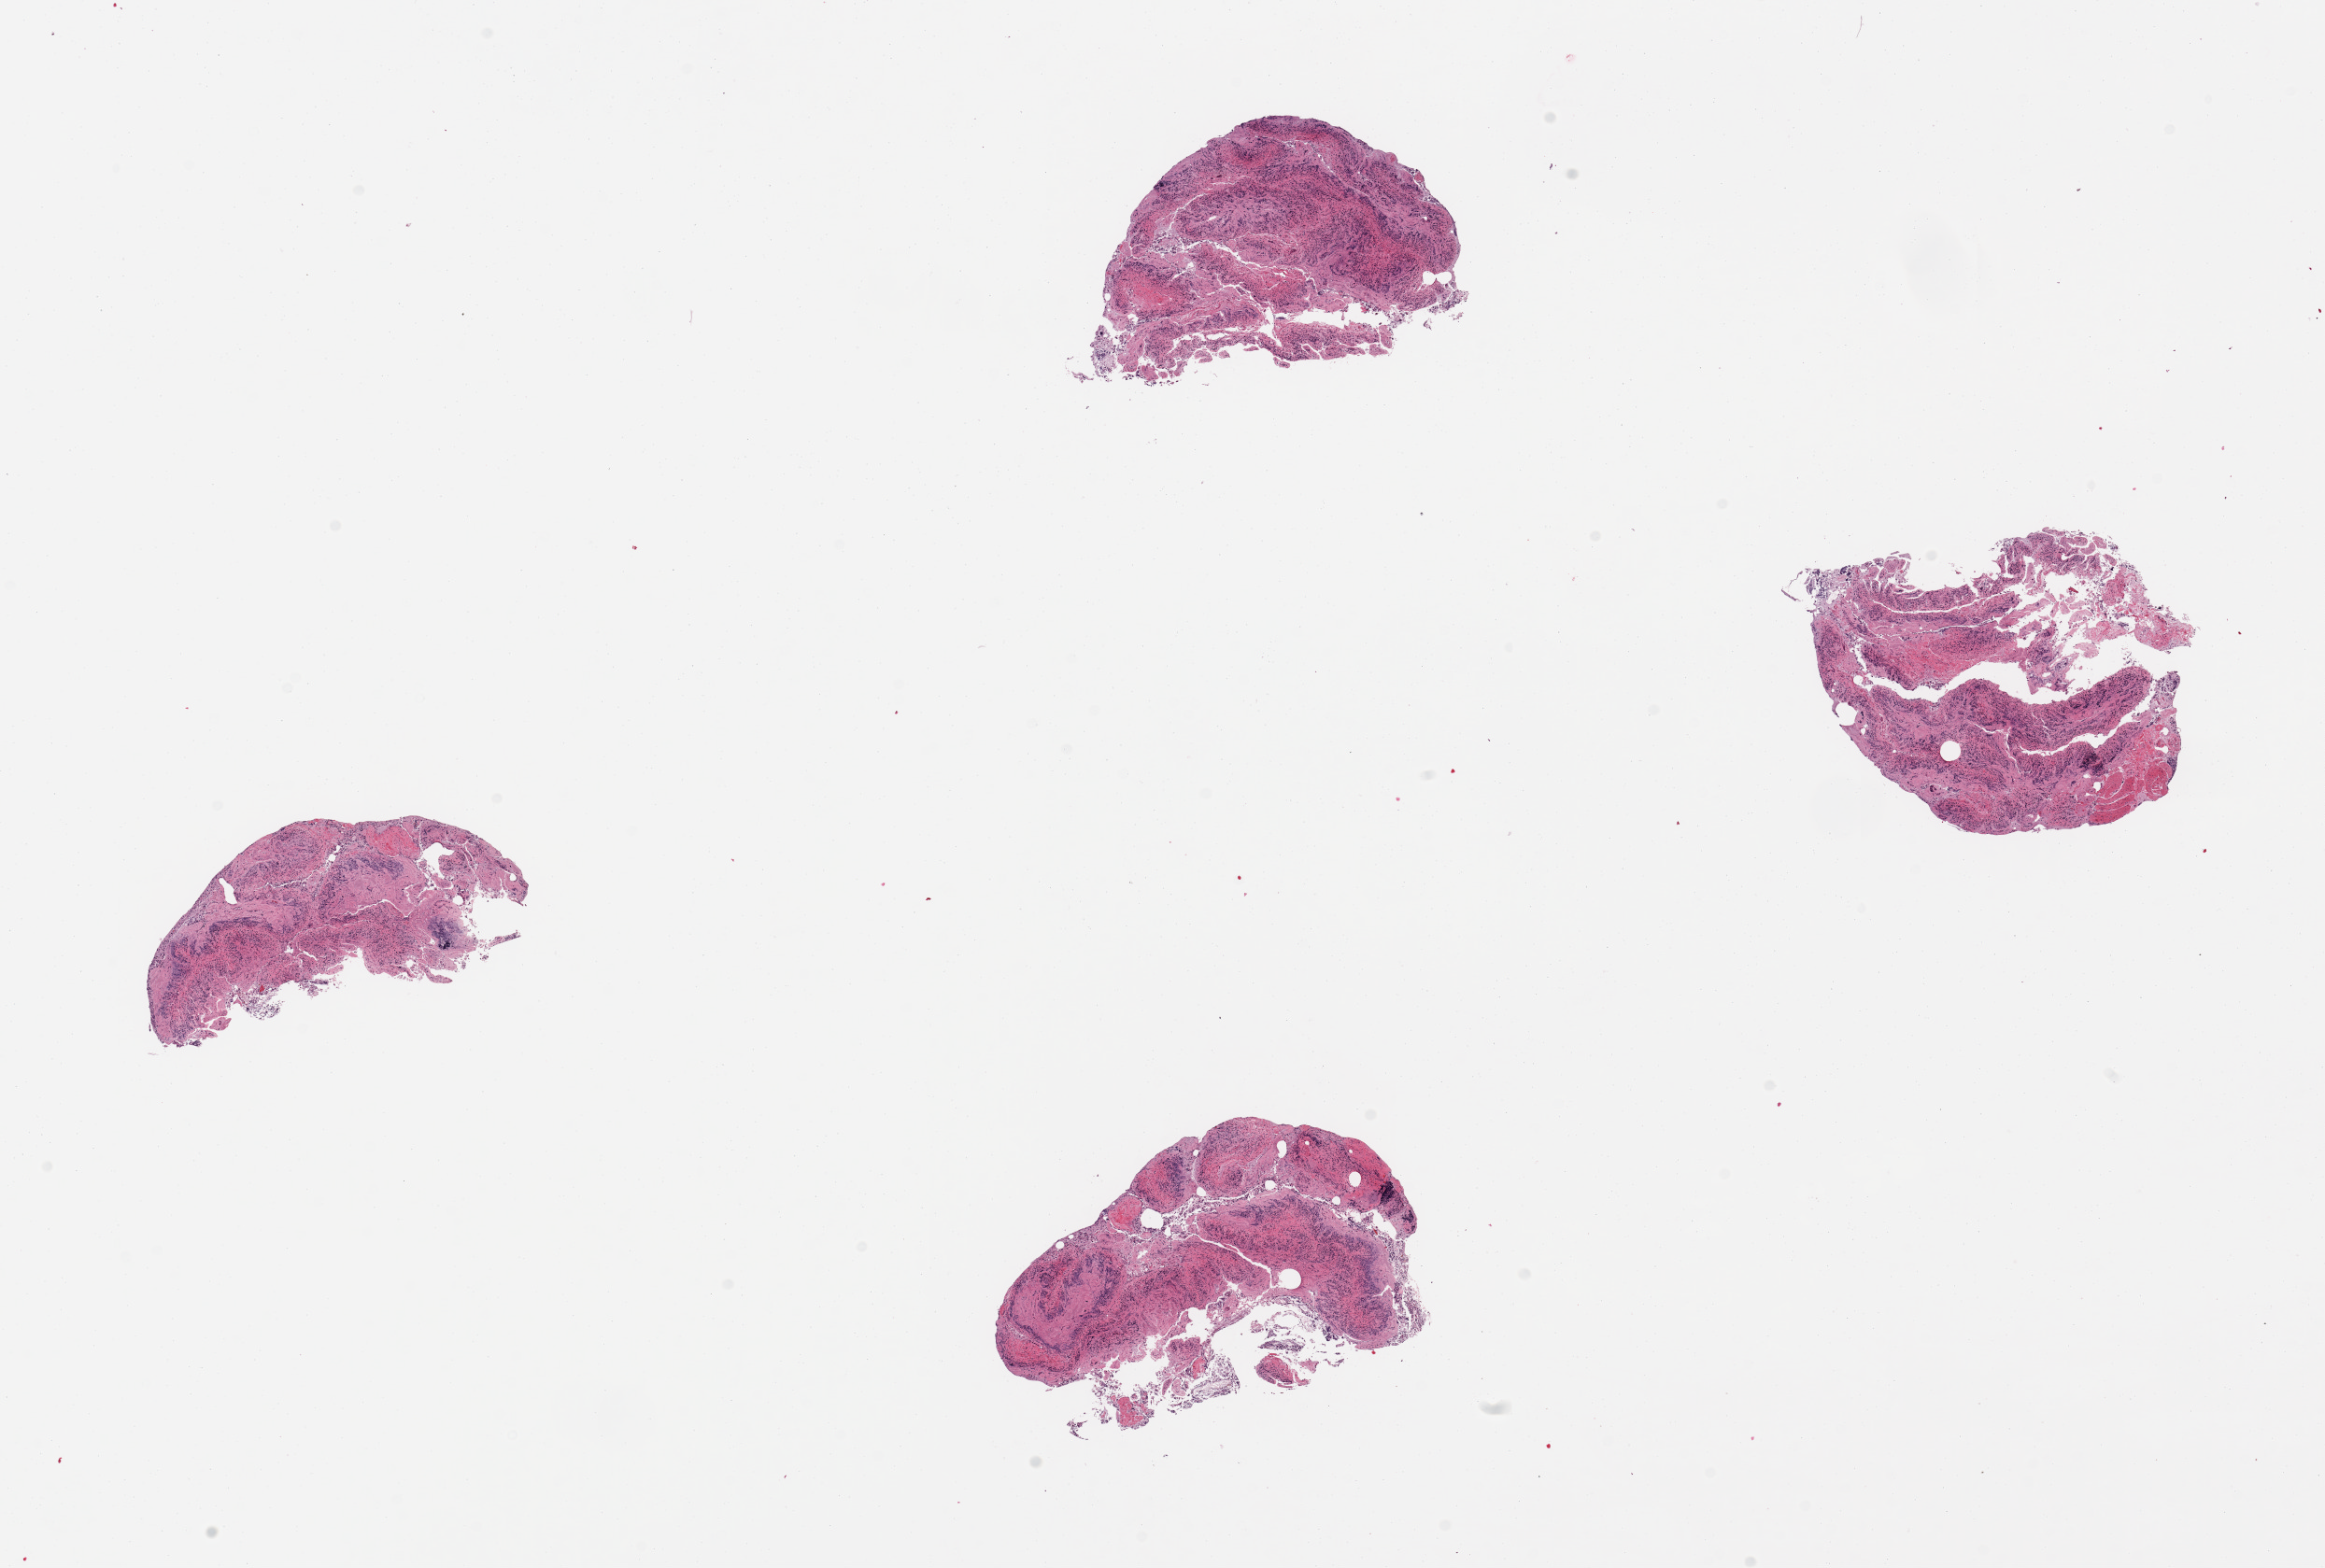
Whole-slide image, H&E stain — low-resolution overview of the scanned area, about 19.7 x 13.3 mm (acquisition: 20x scan); PAXgene-fixed paraffin-embedded (PFPE) section; section of ileum (target tissue); tissue donor sample. Donor sex: male.
Reviewer comment on this tissue sample: 4 pieces; autolyzed.